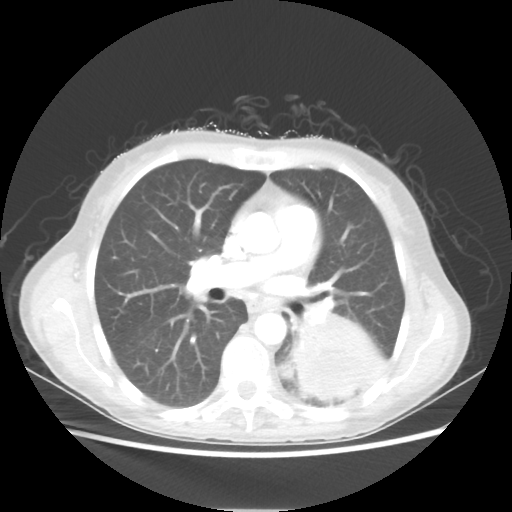
Chest CT, one axial slice; position 31 of 56 along the scan axis; reconstruction kernel STANDARD; 80 kVp; lung window (W 1500 / L -600 HU); 5 mm slice thickness; 512 × 512 image matrix, field of view 360 × 360 mm. Patient: female, 53 years. From the clinical record (not read from this slice): clinical TNM (as recorded): T3 N0 M0.
Outlined on this slice (rectangle marked by the reading radiologist):
- lung tumour (recorded histology: adenocarcinoma): box from (x=295, y=316) to (x=386, y=399) px